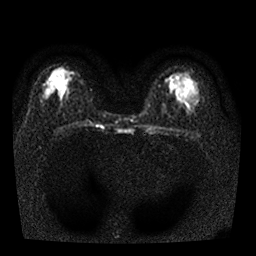
Breast MRI, one axial slice. Slice 15 of 25 in the series (ordered by position). Diffusion-weighted series; image 2 of 4 stored at this slice position (different b-values; order by instance number). 1.5 T. 4 mm slice thickness. 256 × 256 image matrix. Female patient.
Structures marked on this image (outlined manually by an expert reader):
- tumour on diffusion-weighted imaging: bounding box (x1, y1, x2, y2) in pixels: (47, 81, 50, 88)